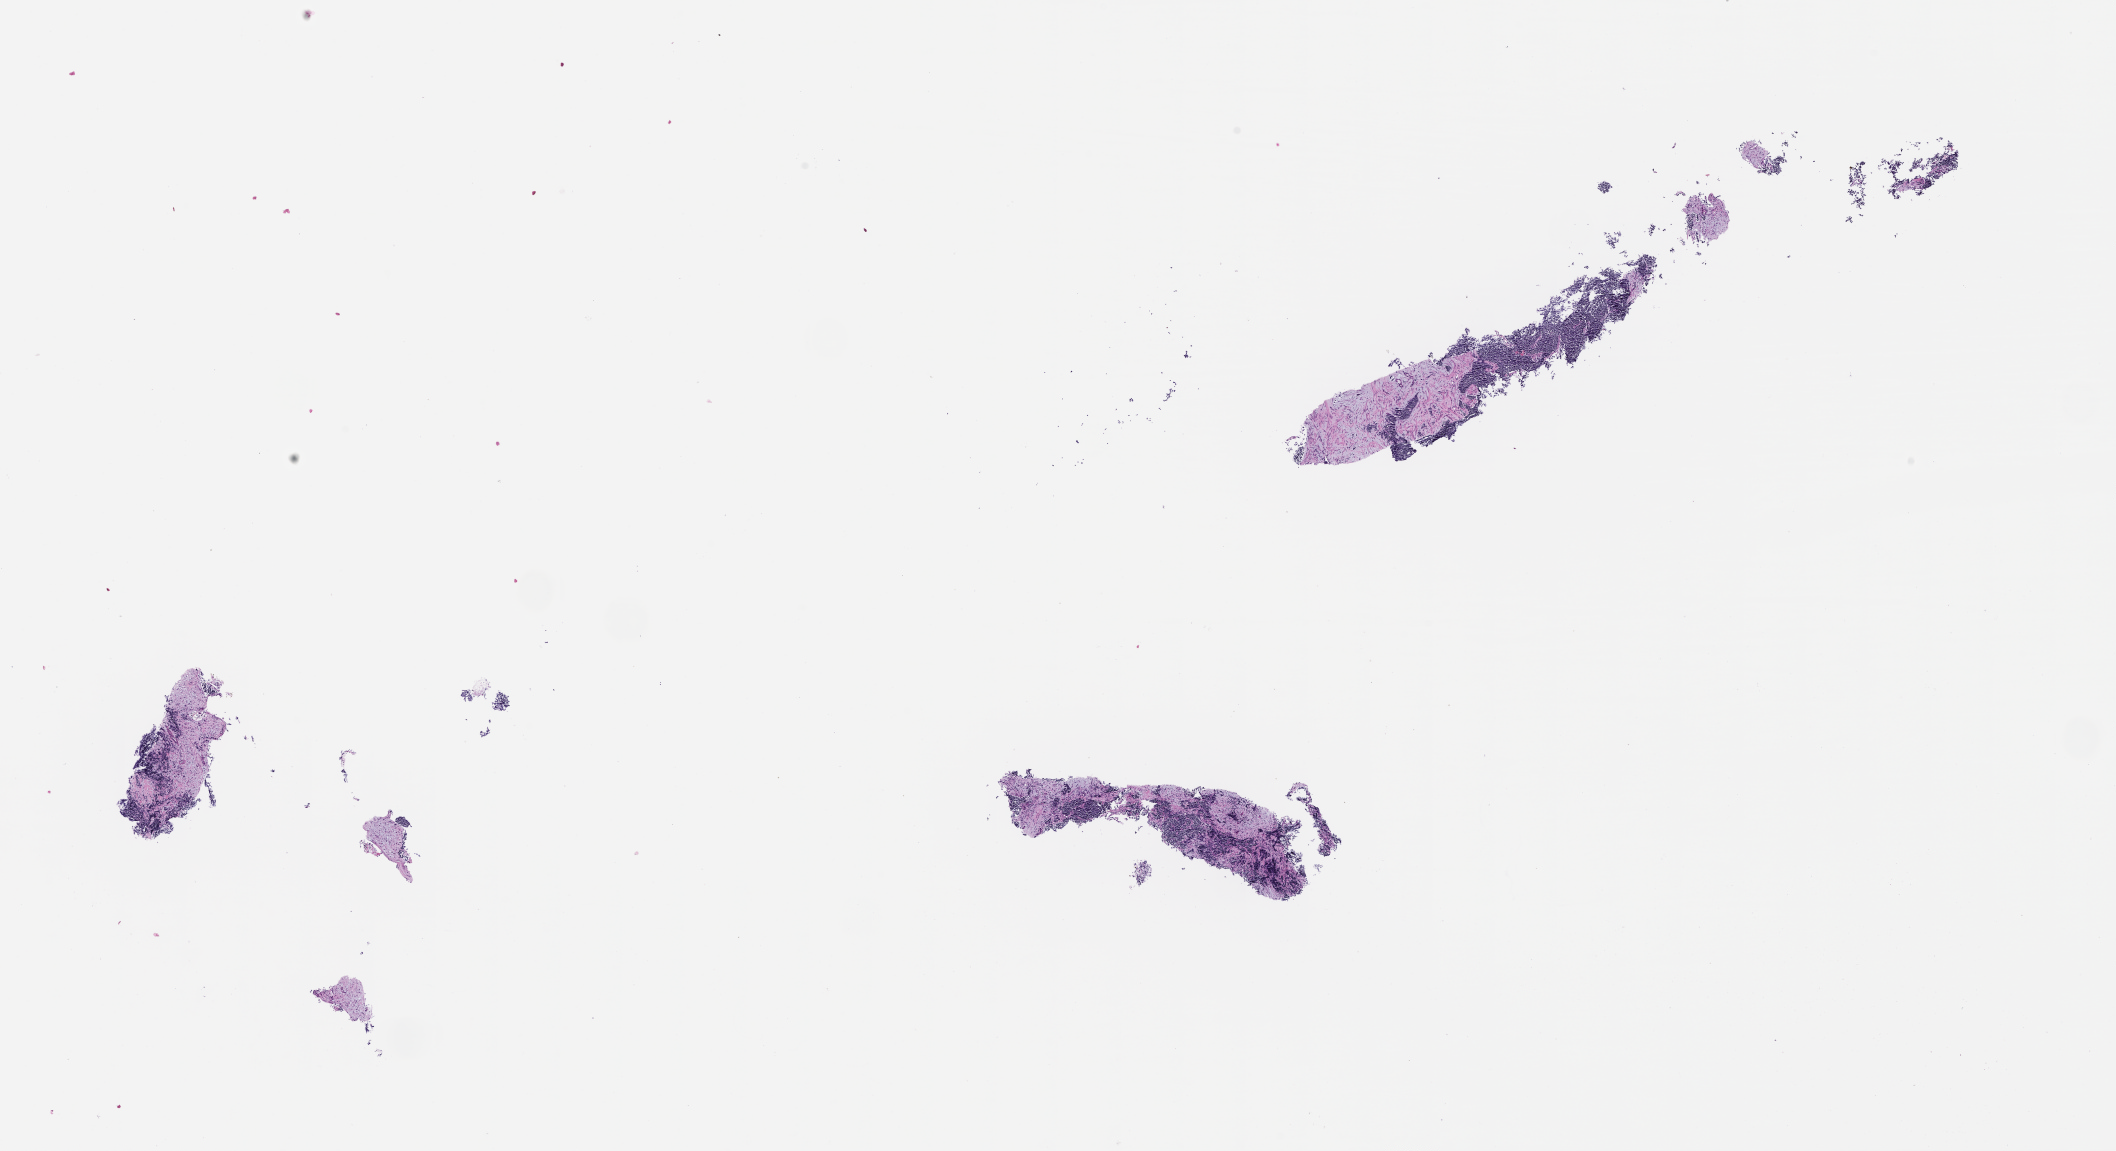
Haematoxylin and eosin whole-slide image, whole scanned area (about 17.1 x 9.3 mm) shown as a low-resolution overview, FFPE section, collected at baseline (before treatment). Patient: male.
This section: metastatic tumor tissue. Primary diagnosis of the patient: Small Cell Lung Carcinoma.